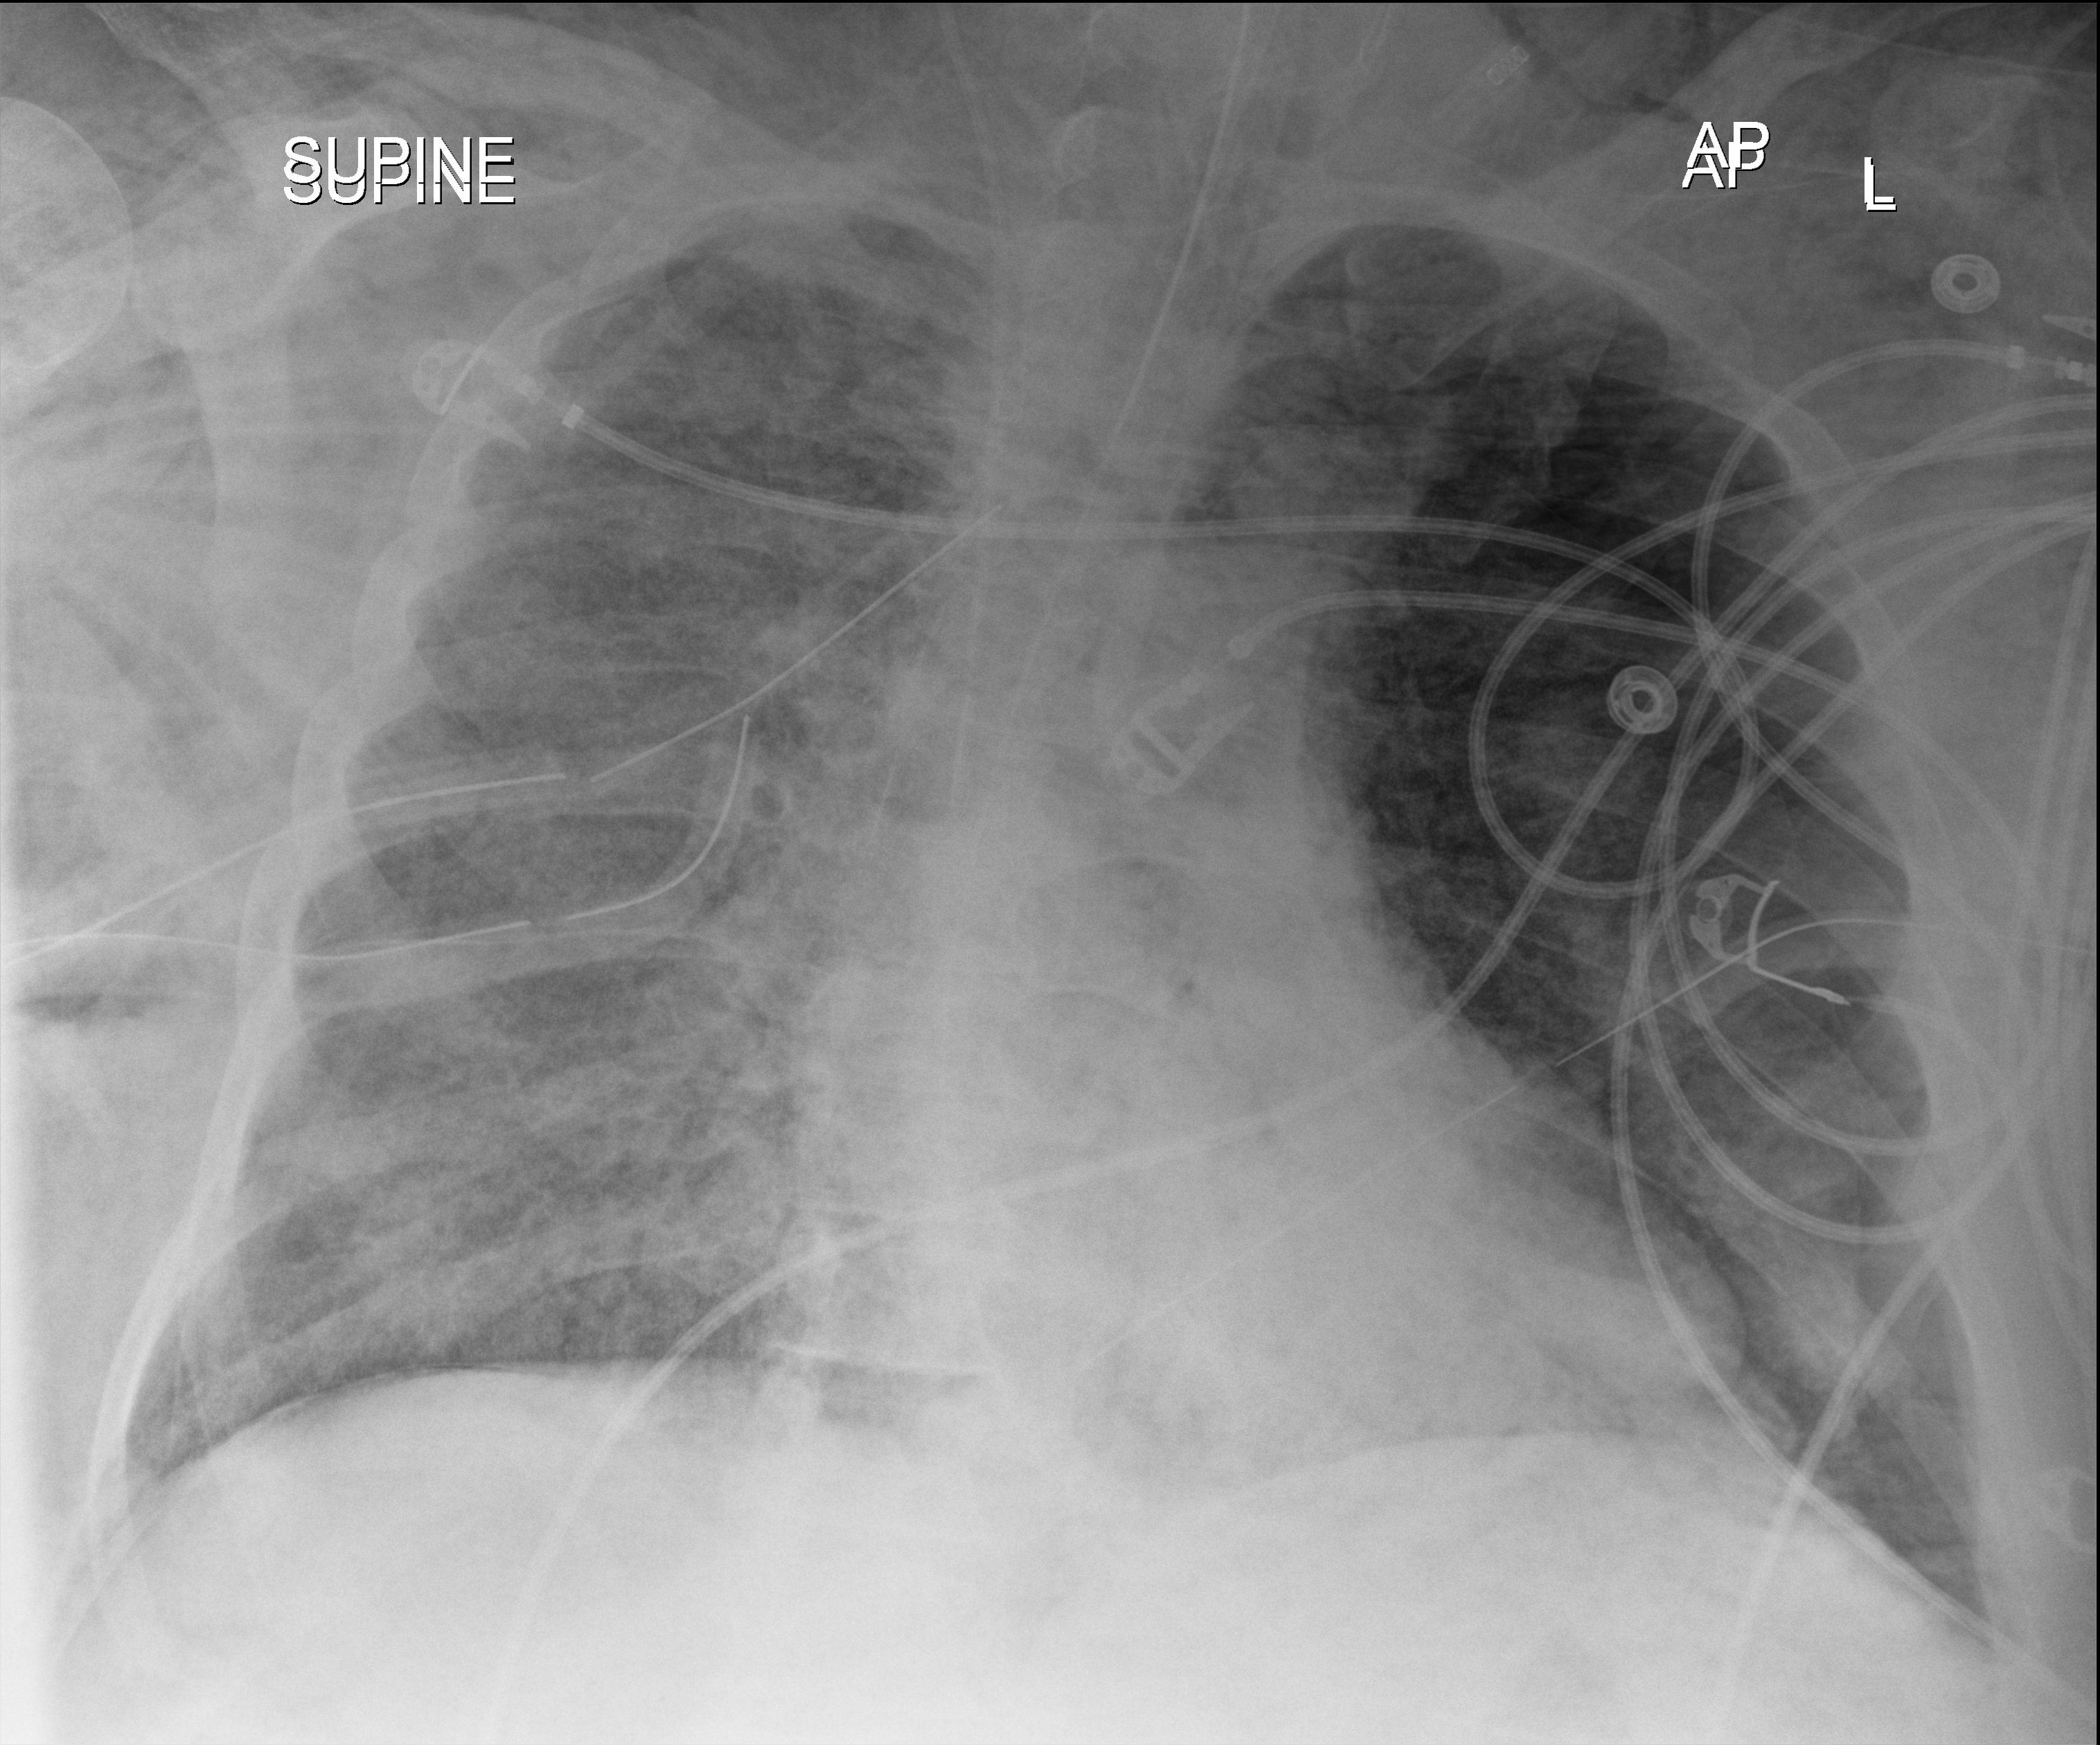
Portable chest radiograph; anteroposterior (AP) projection. Adult patient hospitalised with COVID-19, age 18–59 years.
Admission-level facts for this patient (not findings on this image; timing relative to this image not recorded):
- mechanically ventilated during this hospital stay: yes